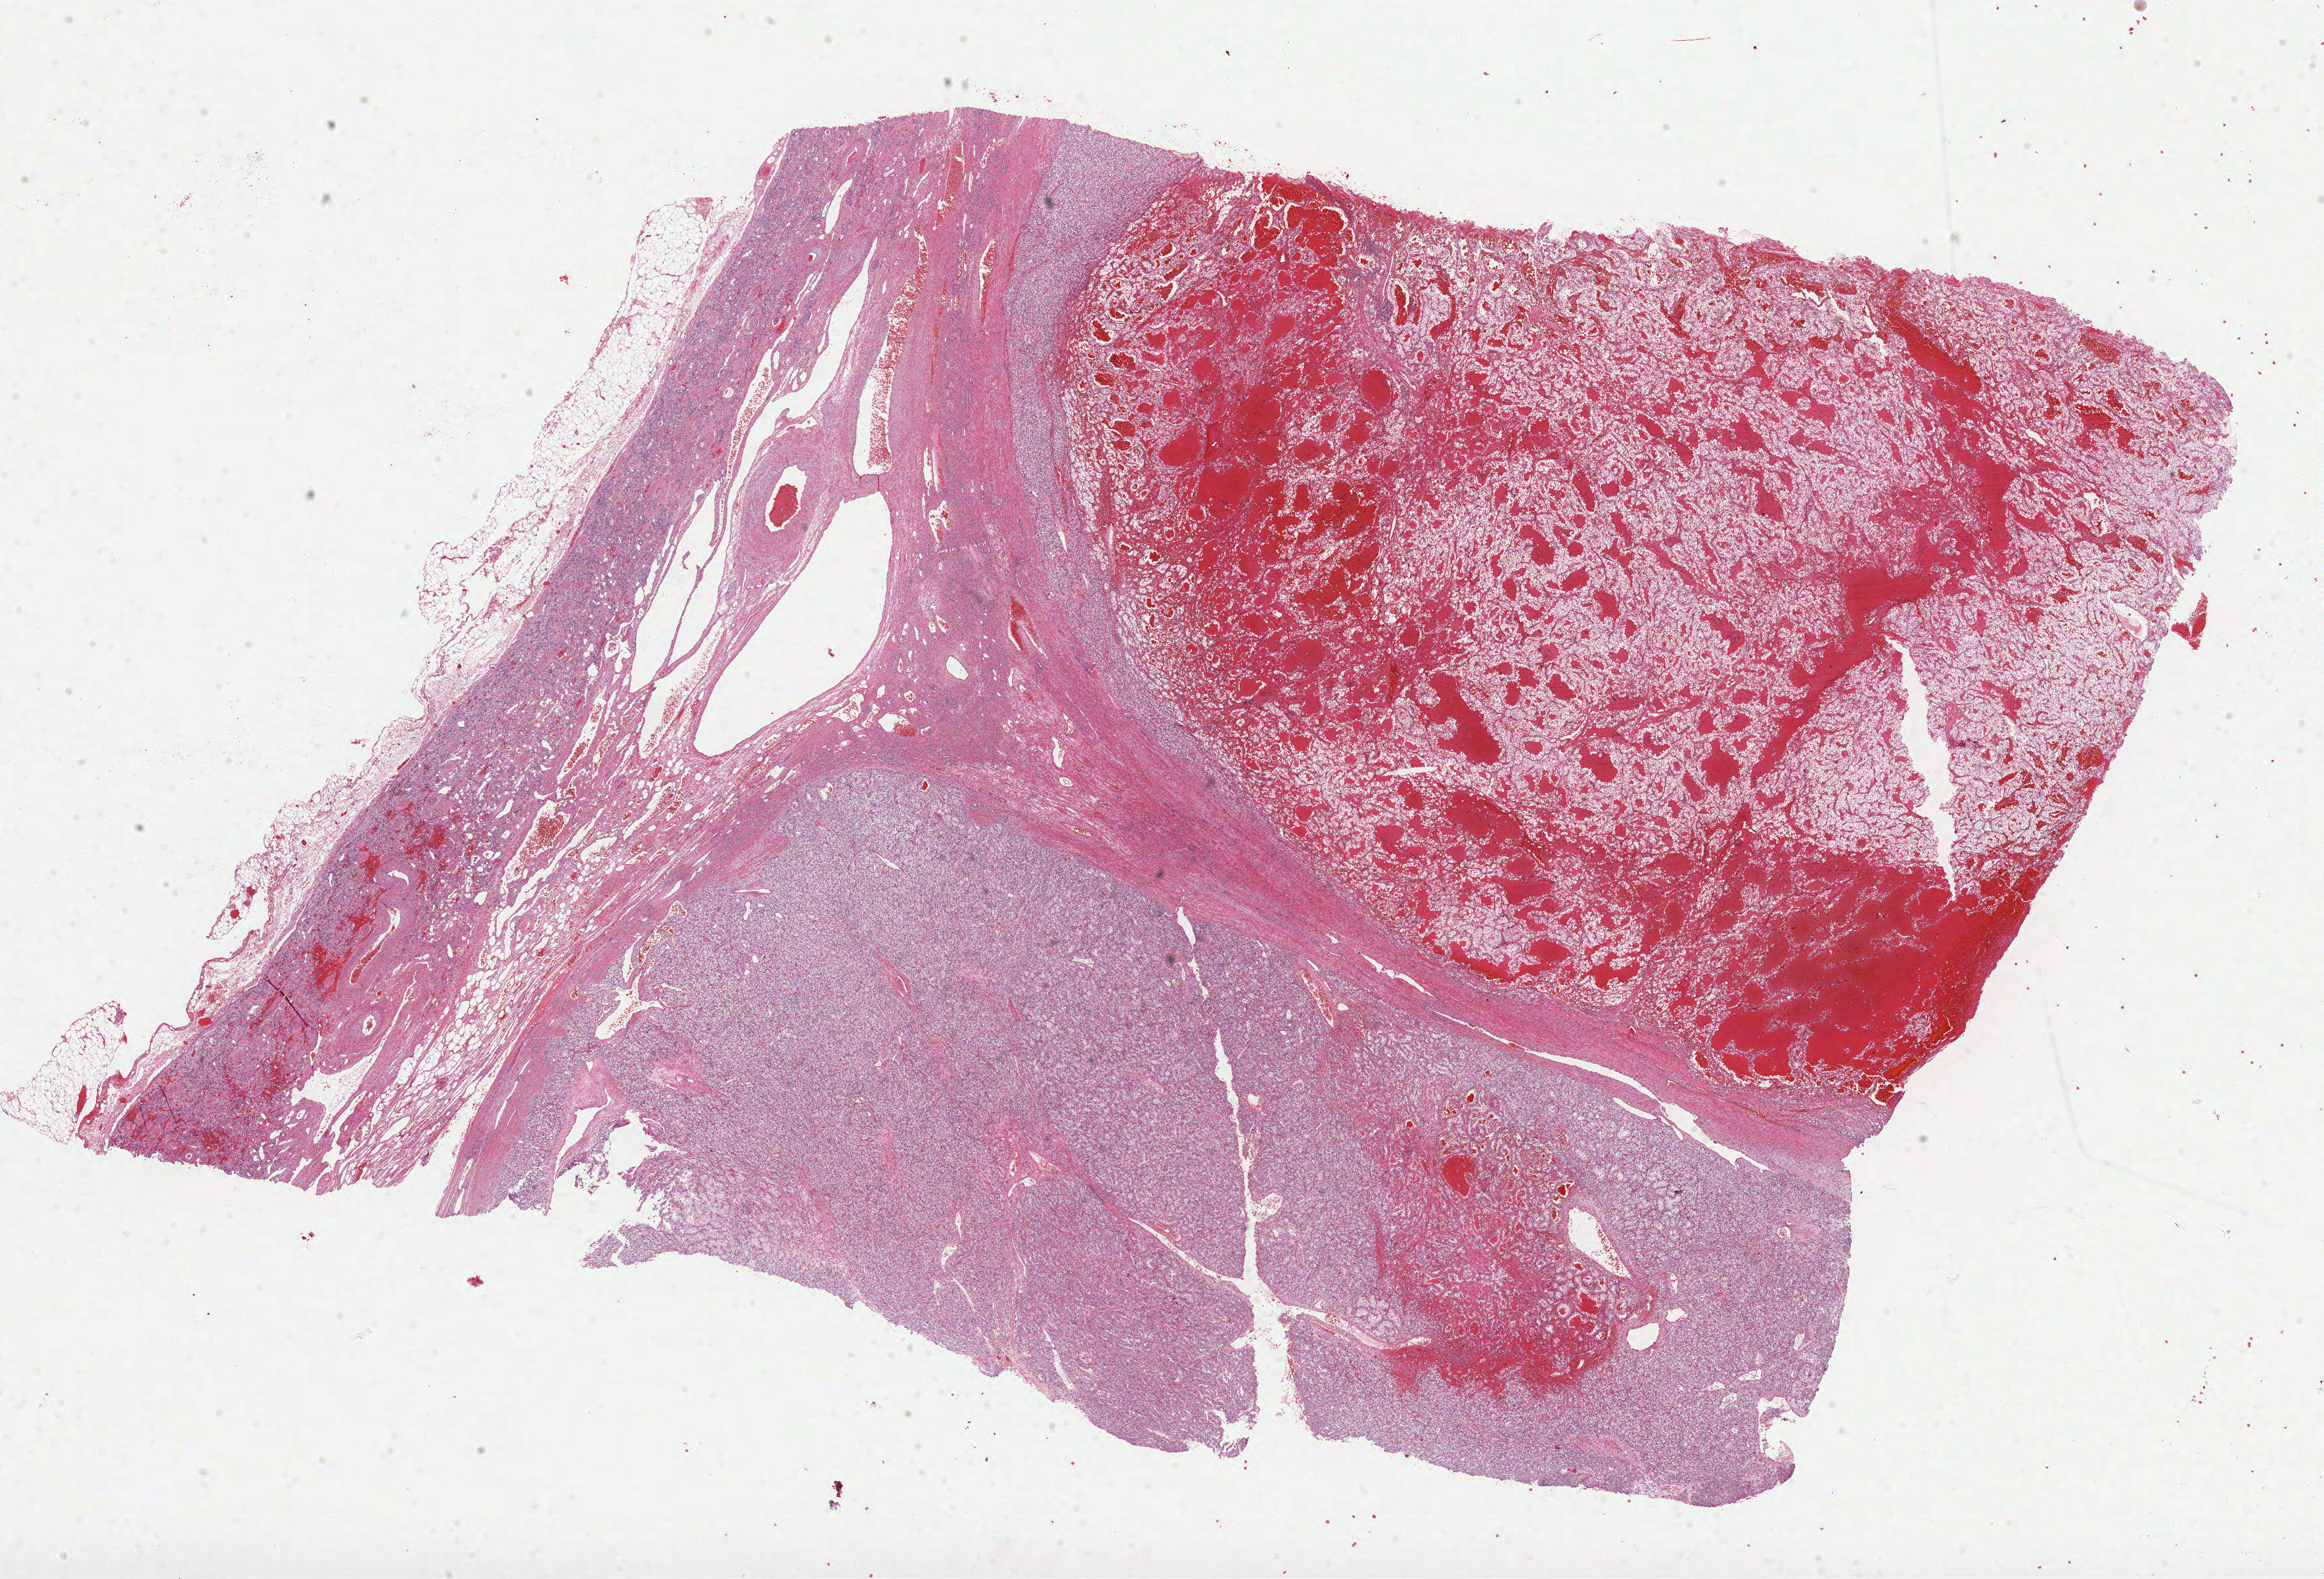
Digitized H&E tissue section (whole slide), shown as a low-resolution overview of the whole scanned area (about 28.5 x 19.4 mm). FFPE section. Kidney, primary tumour sample. Male, age 49 years at initial diagnosis. Histologic grade: G3 (poorly differentiated).
Histologic diagnosis: Clear cell adenocarcinoma, NOS. AJCC pathologic stage: II. TNM: T2 N0 M0. Laterality: left.